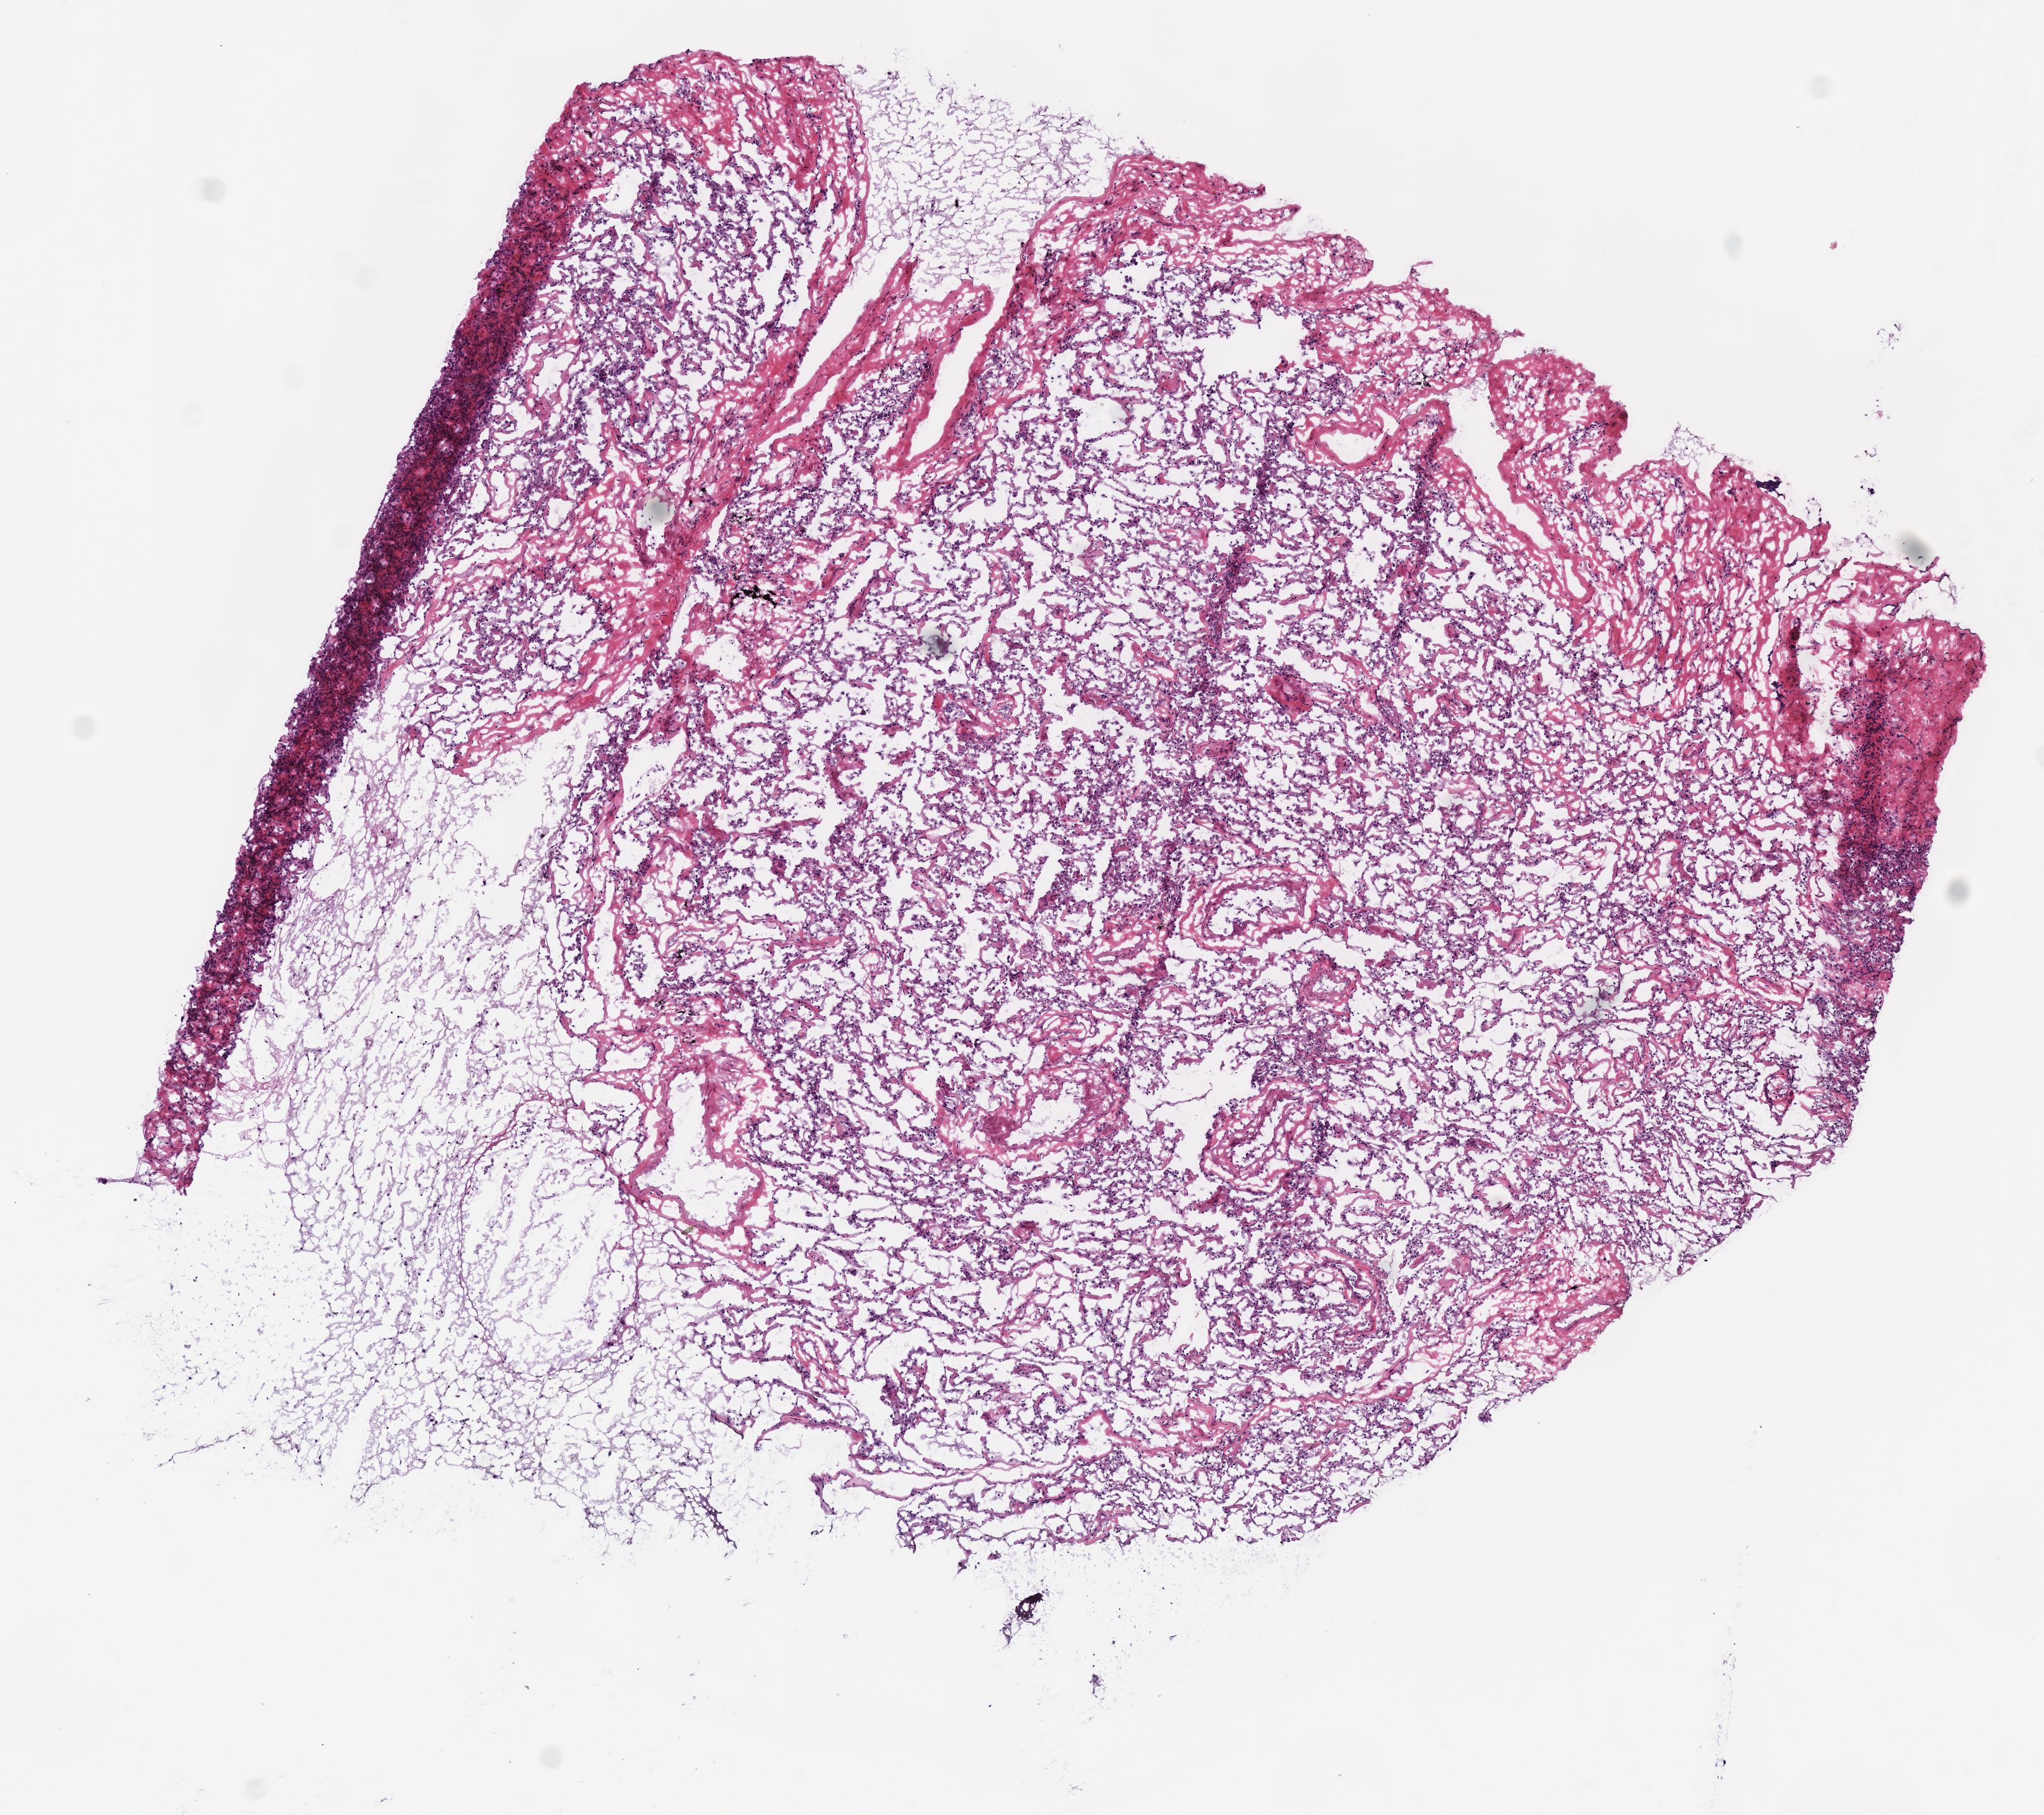
Digitized H&E-stained tissue section (whole slide), low-resolution overview of the scanned area, about 6.4 x 5.7 mm; frozen section; sample: solid tissue normal (non-tumour tissue), lung. Female, age 64 years at initial diagnosis.
This section: solid tissue normal (non-tumour) sample from the same patient. Patient diagnosis: Mucinous adenocarcinoma (upper lobe, lung).